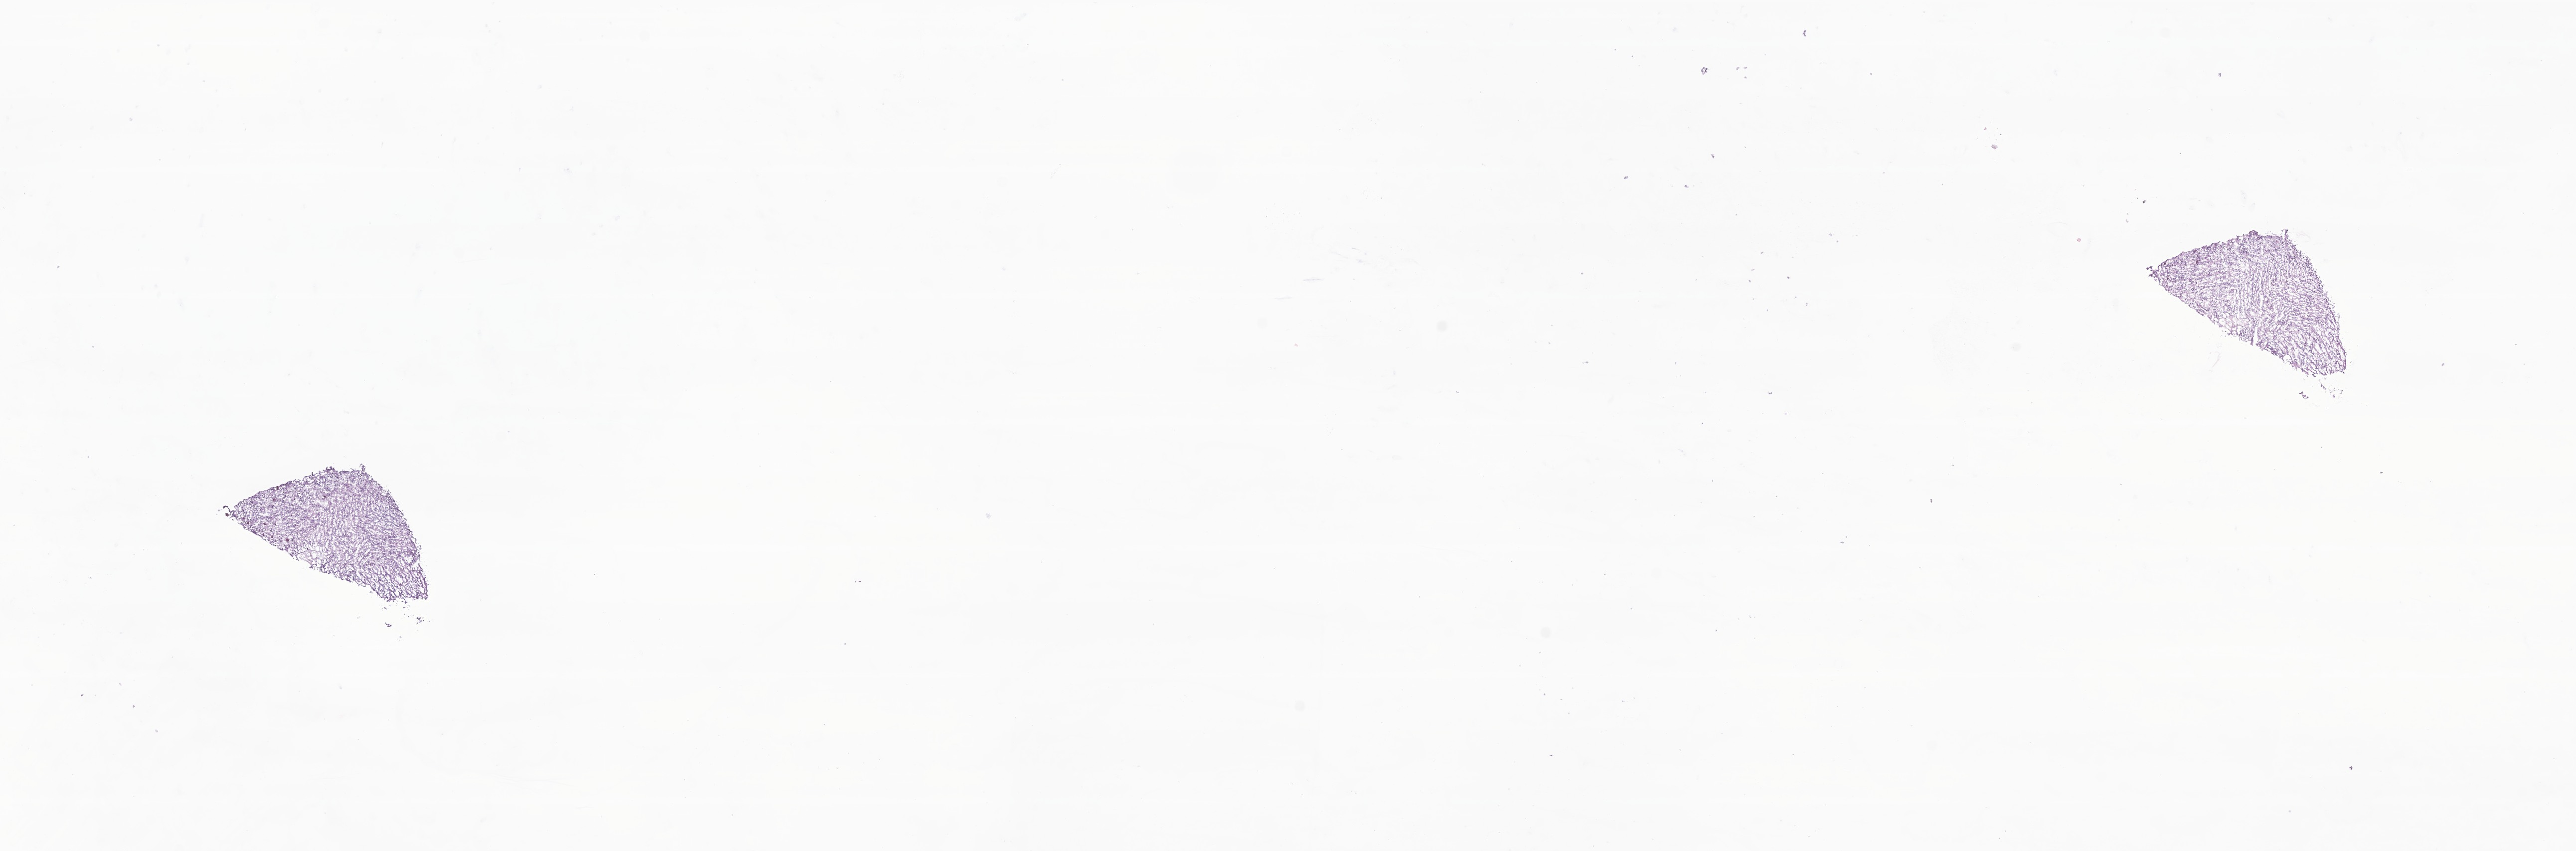
Digitized hematoxylin and eosin (H&E)-stained section of tumor tissue from the frontal lobe, low-resolution overview of the scanned area, about 21.8 x 7.2 mm. Frozen section (OCT-embedded). Patient: female, age 69 months (5 years 9 months).
- diagnosis: Ependymoma, anaplastic